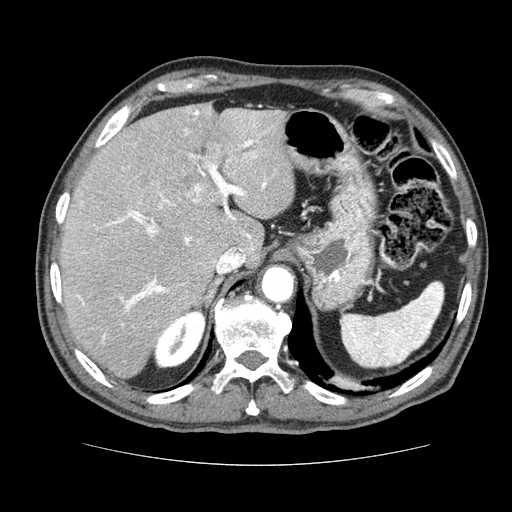
Contrast-enhanced abdominal CT (liver protocol), one axial slice. Soft-tissue window (W 400 / L 40 HU). 2.5 mm slice thickness. 512 × 512 image matrix, field of view 360 × 360 mm. Case-level facts recorded for this patient, not image findings: diagnosis: hepatocellular carcinoma (patient treated with transarterial chemoembolisation; whether this scan precedes or follows treatment is not stated here); TNM stage (as recorded): Stage-I; Child-Pugh class: A; tumour nodularity: uninodular.
Outlined on this slice (semi-automatic segmentation, software-assisted and operator-edited):
- liver parenchyma outside the tumour (the mass and vessels are separate outlines, so this box may not span the whole liver): box from (x=60, y=104) to (x=294, y=378) px
- liver vessels: (x=76, y=110)–(x=267, y=340)